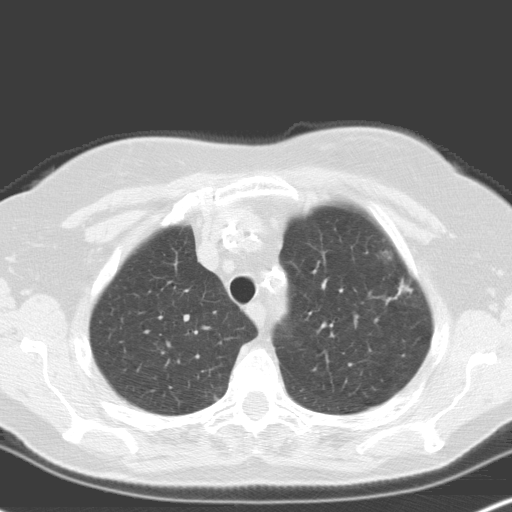
Low-dose screening chest CT, one axial slice; slice 135 of 160 in the series (ordered by position); lung window (W 1500 / L -600 HU); 3.2 mm slice thickness; 512 × 512 image matrix, field of view 316 × 316 mm.
Annotated regions visible in this slice (expert manual segmentation):
- lesion 2 (nodule): bounding box [x1, y1, x2, y2] px = [395, 284, 413, 298]